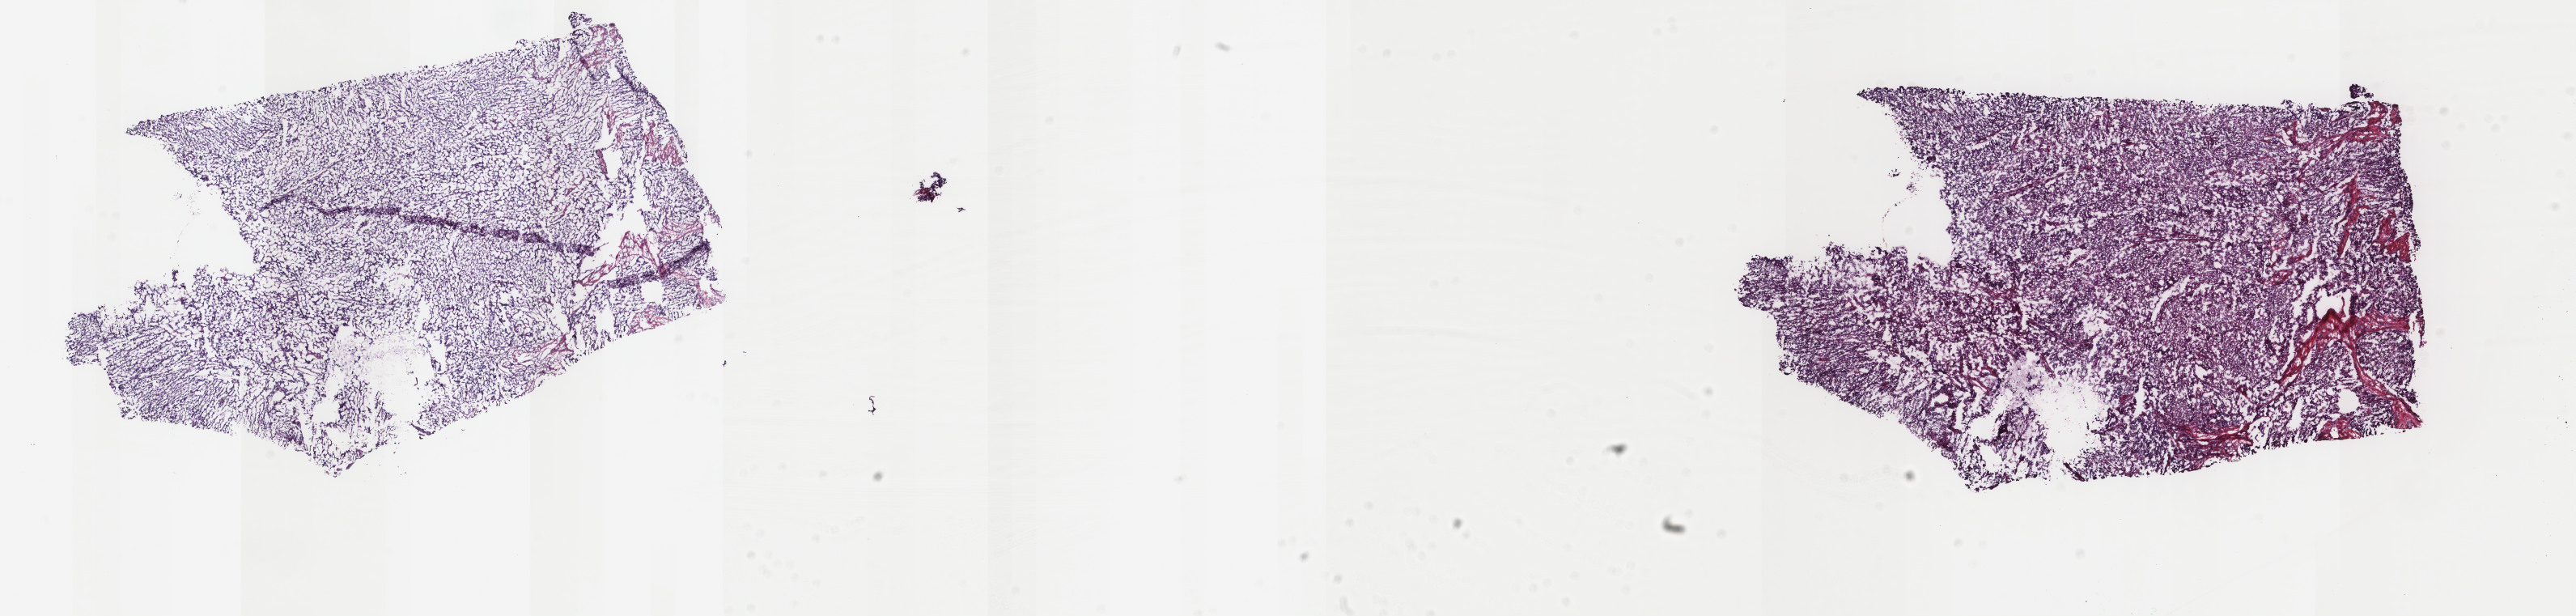
Digitized H&E-stained tissue section (whole slide) — whole scanned area (about 25.3 x 6.0 mm, from a 40x scan) shown as a low-resolution overview, frozen section, uterus, primary tumour sample. Female, age 69 years at initial diagnosis. Composition of this section per pathologist review: tumour cells 92%, tumour nuclei 96%.
Histologic diagnosis: Endometrioid adenocarcinoma, NOS.